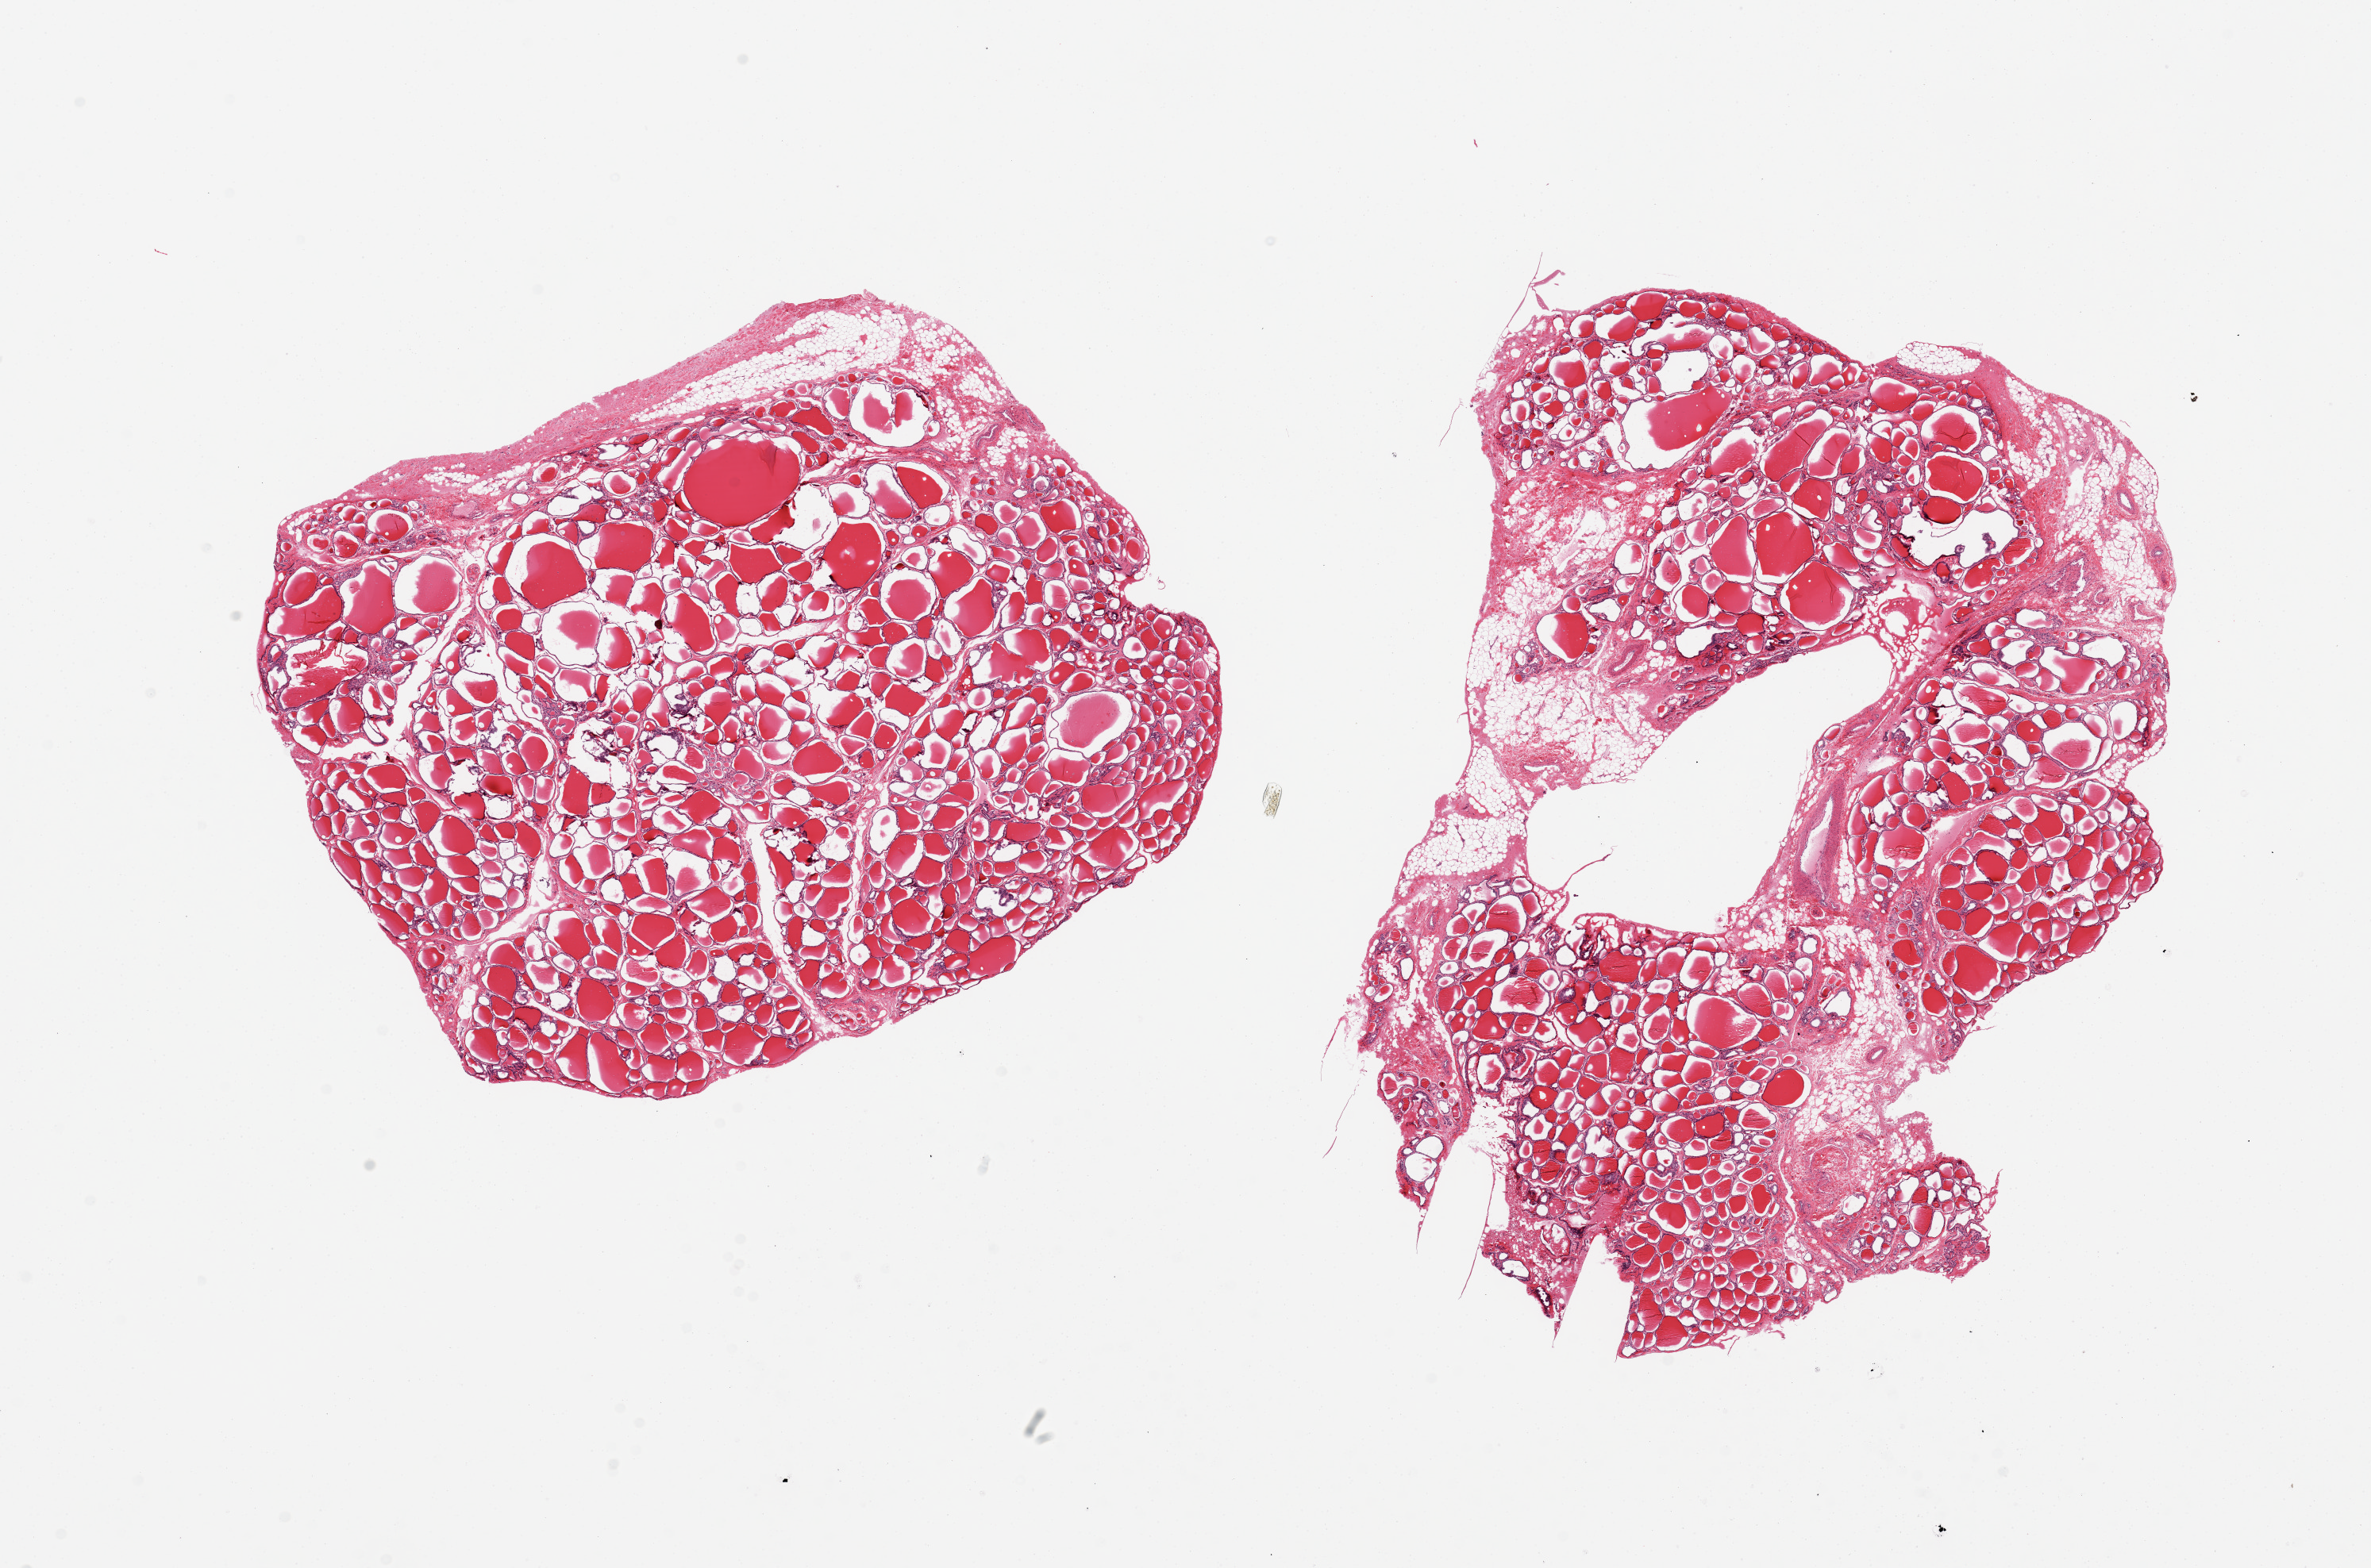
Digitized haematoxylin and eosin-stained section, shown as a low-resolution overview of the whole scanned area (about 23.6 x 15.6 mm); PAXgene-fixed, paraffin-embedded tissue; target tissue: thyroid; tissue donor sample. Donor: male.
- pathologist's review note for this sample: 2 pieces, regressive areas, adherent fat/fibrous tags